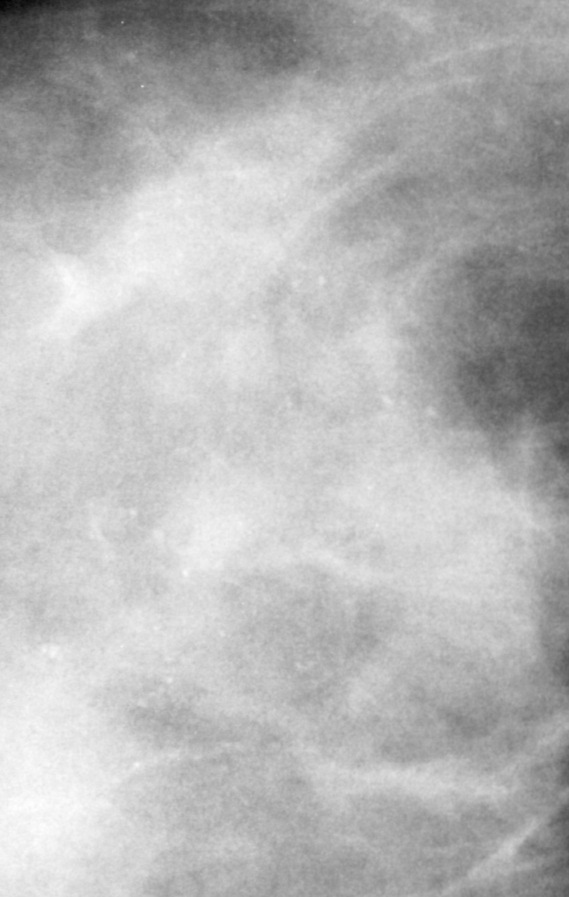
Region of interest cut from a scanned film mammogram (one marked finding), left breast, CC view.
Finding: calcifications, morphology punctate, distribution segmental; BI-RADS assessment category 4; pathology (as recorded): benign.